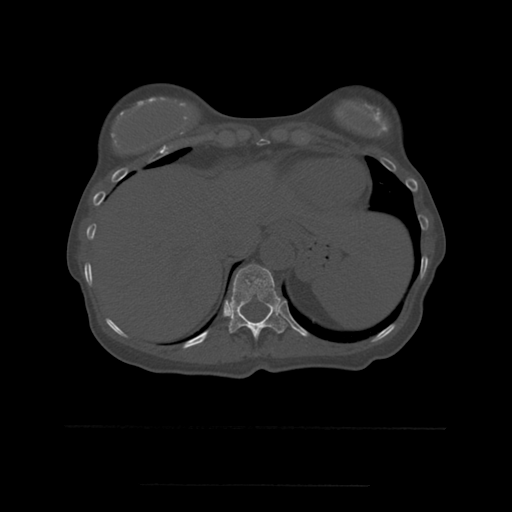
CT including the spine, one axial slice; slice 283 of 544 in the series (ordered by position); bone window (W 1800 / L 400 HU); 1.25 mm slice thickness; 512 × 512 image matrix, field of view 350 × 350 mm. Patient age 58 years. From the clinical record (not read from this slice): primary cancer: lung.
Outlined on this slice (semi-automatically segmented with operator editing):
- T11 vertebra: bounding box (x1, y1, x2, y2) in pixels: (228, 265, 287, 340)